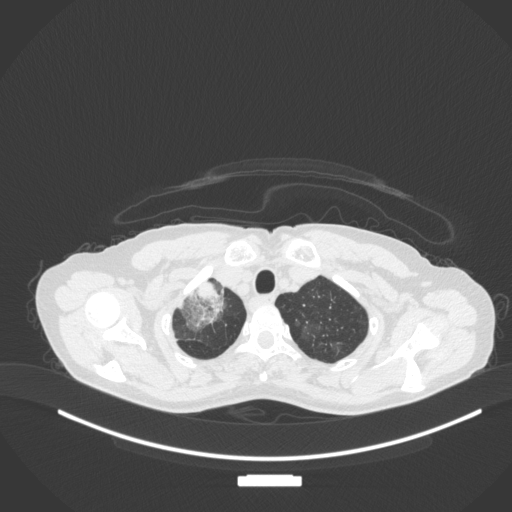
Chest CT, one axial slice. Position 290 of 311 along the scan axis. Reconstruction kernel B31f. 120 kVp. Lung window (W 1500 / L -600 HU). 1 mm slice thickness. 512 × 512 image matrix. Female patient, age 59 years. Case-level facts recorded for this patient, not image findings: clinical TNM (as recorded): T3 N0 M0.
Structures marked on this image (rectangle marked by the reading radiologist):
- lung tumour (recorded histology: adenocarcinoma): bounding box [x1, y1, x2, y2] px = [179, 279, 229, 334]